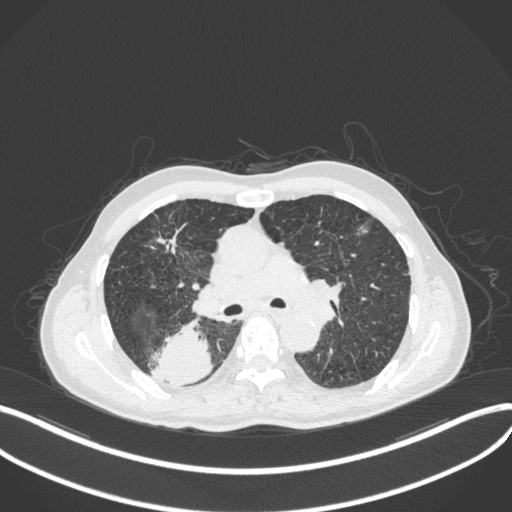
Chest CT, one axial slice. Slice 279 of 423 in the series (ordered by position). Reconstruction kernel B31f. 120 kVp. Lung window (W 1500 / L -600 HU). 1 mm slice thickness. 512 × 512 image matrix. Male patient, age 79 years. Case-level facts recorded for this patient, not image findings: clinical TNM (as recorded): T3 N0 M0.
Outlined on this slice (bounding box drawn by a radiologist):
- lung tumour (recorded histology: adenocarcinoma): bounding box (x1, y1, x2, y2) in pixels: (147, 316, 216, 388)